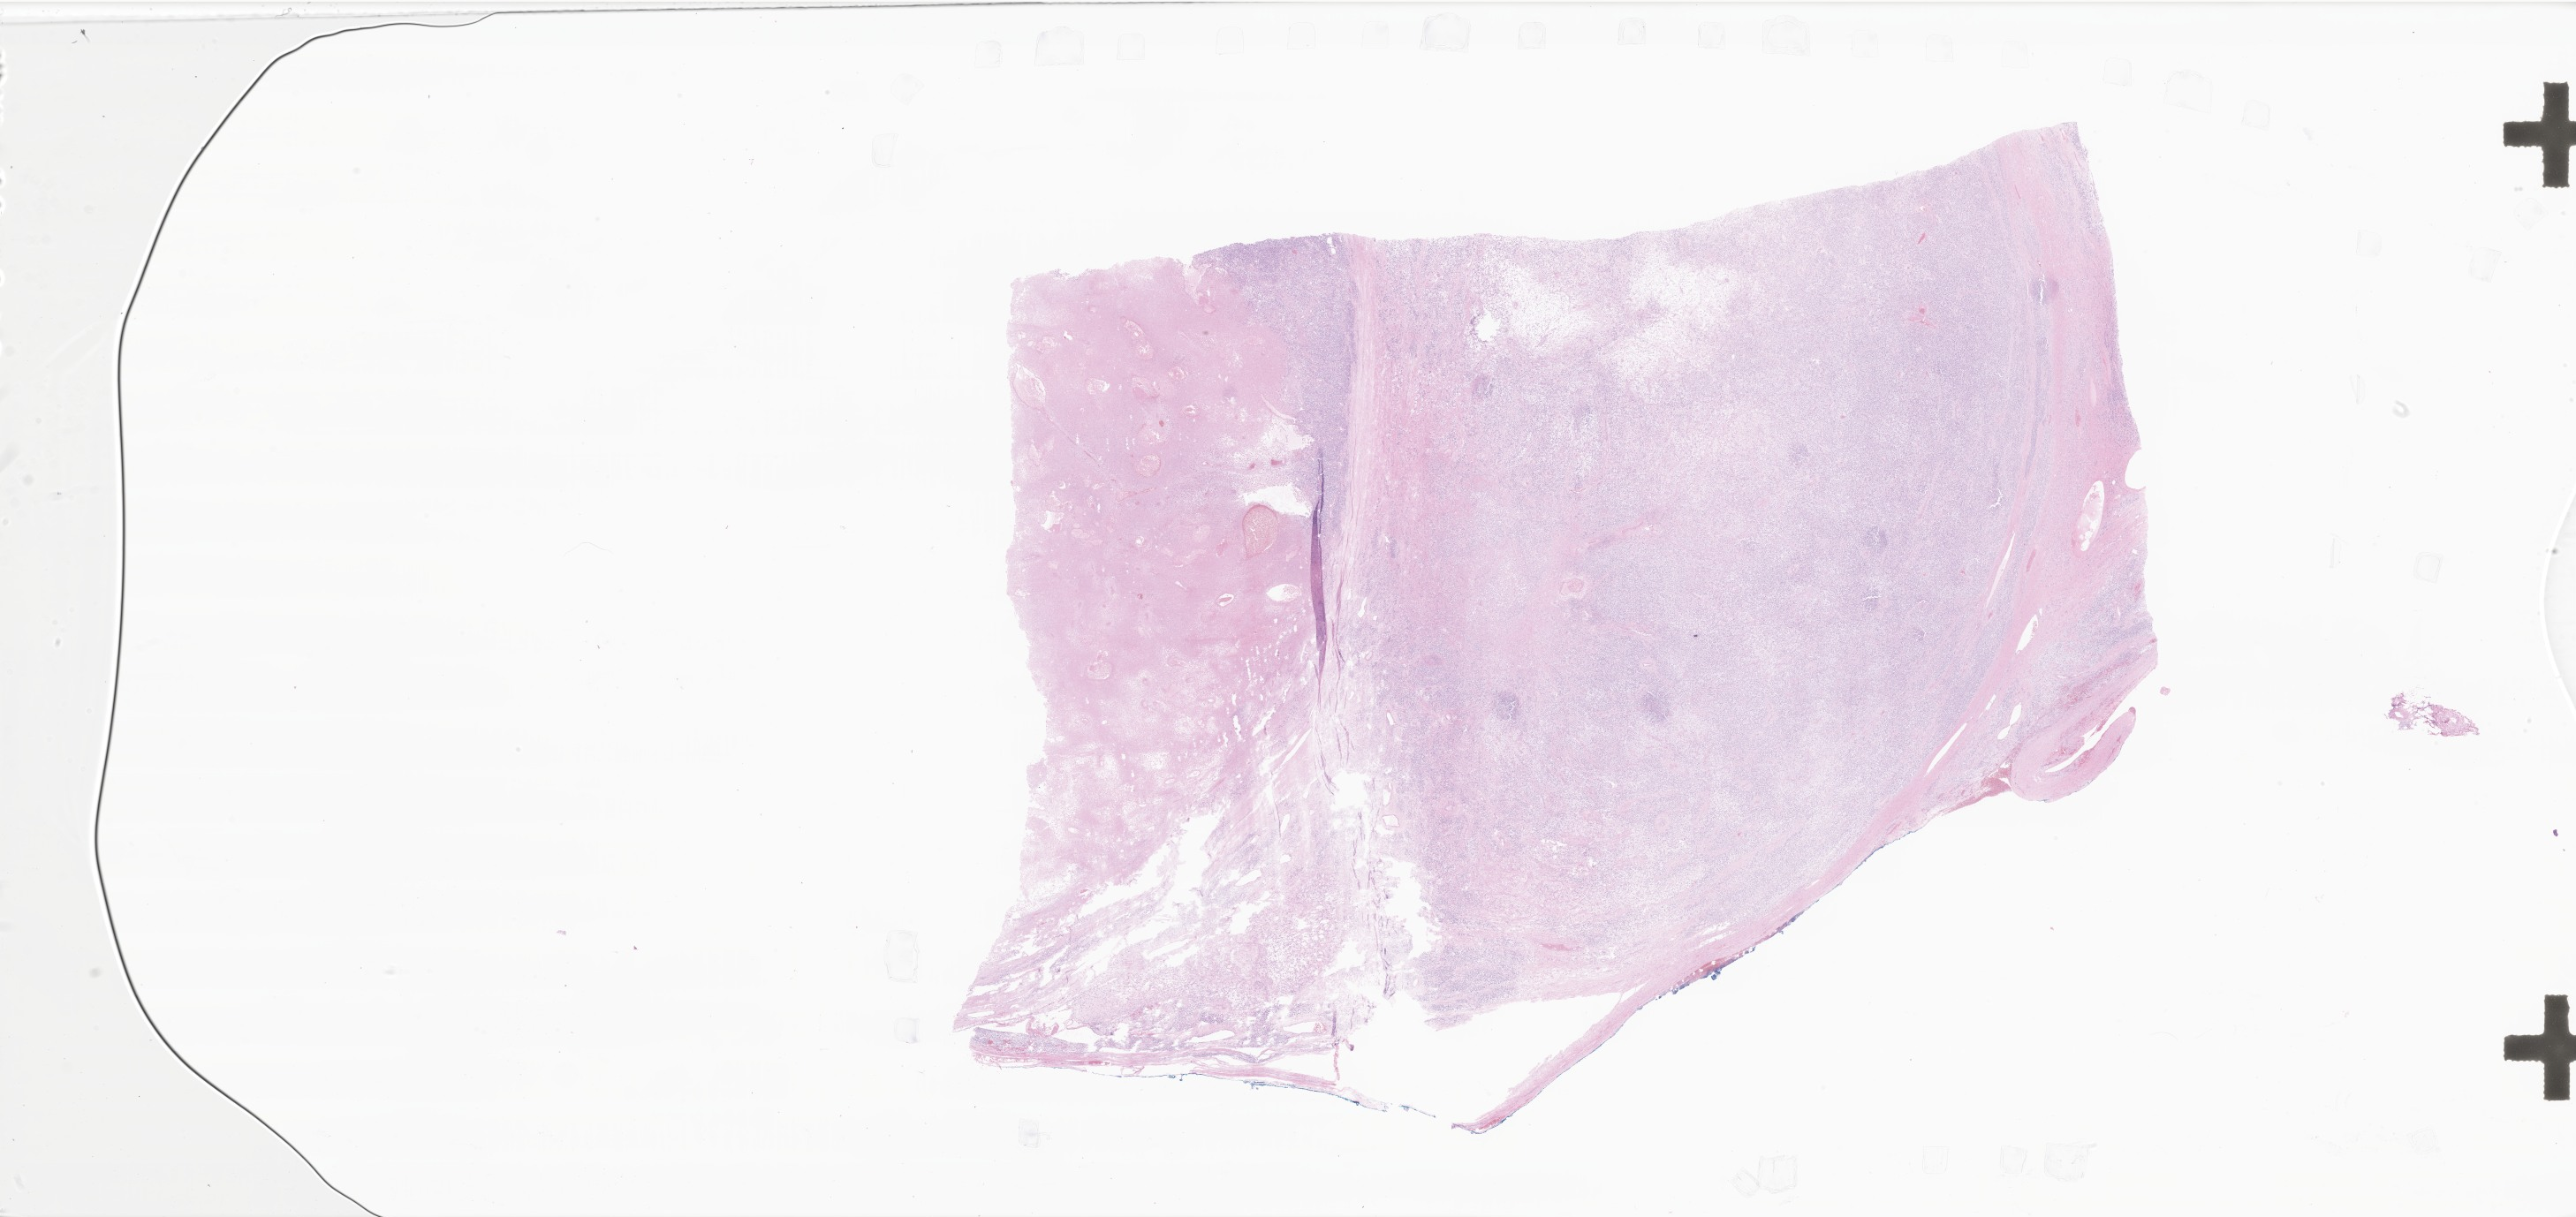
H&E whole-slide image of tumor tissue from the testis — a low-resolution overview of the entire scanned area, about 49.2 x 23.2 mm. FFPE section. Patient male; age 227 months (18 years 11 months).
Diagnosis: Embryonal rhabdomyosarcoma, NOS.